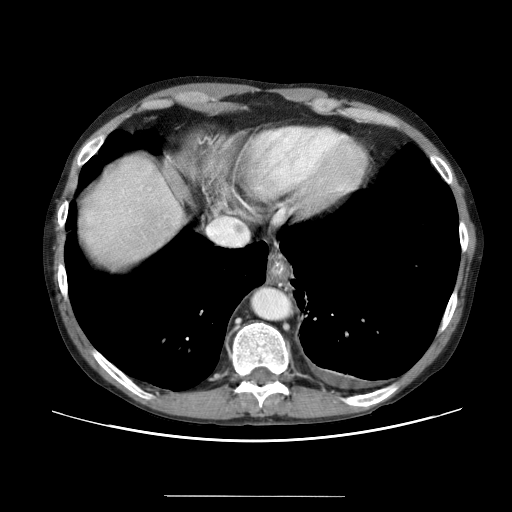
Contrast-enhanced abdominal CT (liver protocol), one axial slice; slice 57 of 69 in the series (ordered by position); reconstruction kernel STANDARD; 120 kVp; soft-tissue window (W 400 / L 40 HU); 2.5 mm slice thickness; 512 × 512 image matrix. Case-level facts recorded for this patient, not image findings: diagnosis: hepatocellular carcinoma (patient treated with transarterial chemoembolisation; whether this scan precedes or follows treatment is not stated here); TNM stage (as recorded): Stage-IVB; Child-Pugh class: B.
Outlined on this slice (semi-automatically segmented with operator editing):
- liver parenchyma outside the tumour (the mass and vessels are separate outlines, so this box may not span the whole liver): bounding box [x1, y1, x2, y2] px = [74, 130, 248, 288]
- liver vessels: [138, 196, 140, 198]